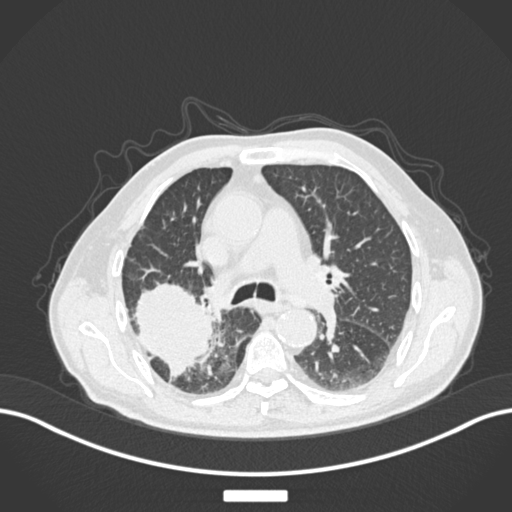
Chest CT, one axial slice. Slice 109 of 201 in the series (ordered by position). Reconstruction kernel B30f. 120 kVp. Lung window (W 1500 / L -600 HU). 1 mm slice thickness. 512 × 512 image matrix, field of view 400 × 400 mm. Male patient, age 72 years. Case-level facts recorded for this patient, not image findings: clinical TNM (as recorded): T3 N2 M0.
Annotated regions visible in this slice (rectangle marked by the reading radiologist):
- lung tumour (recorded histology: adenocarcinoma): bounding box <132,277,217,378> (left, top, right, bottom; pixels)